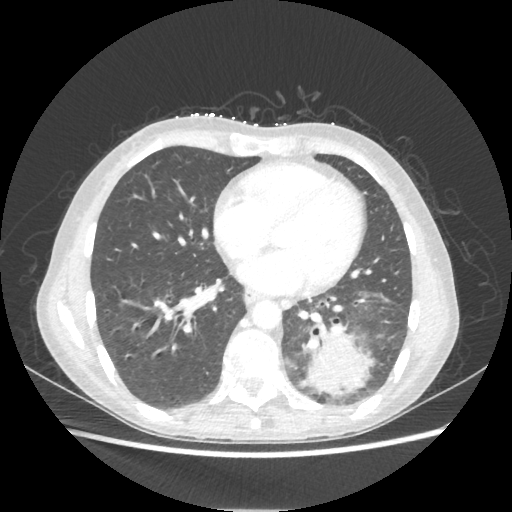
Chest CT, one axial slice; slice 89 of 221 in the series (ordered by position); reconstruction kernel STANDARD; lung window (W 1500 / L -600 HU); 1.25 mm slice thickness; 512 × 512 image matrix, field of view 360 × 360 mm. Female patient, age 53 years. Case-level facts recorded for this patient, not image findings: clinical TNM (as recorded): T3 N0 M0.
Structures marked on this image (rectangle marked by the reading radiologist):
- lung tumour (recorded histology: adenocarcinoma): bounding box <299,326,373,395> (left, top, right, bottom; pixels)